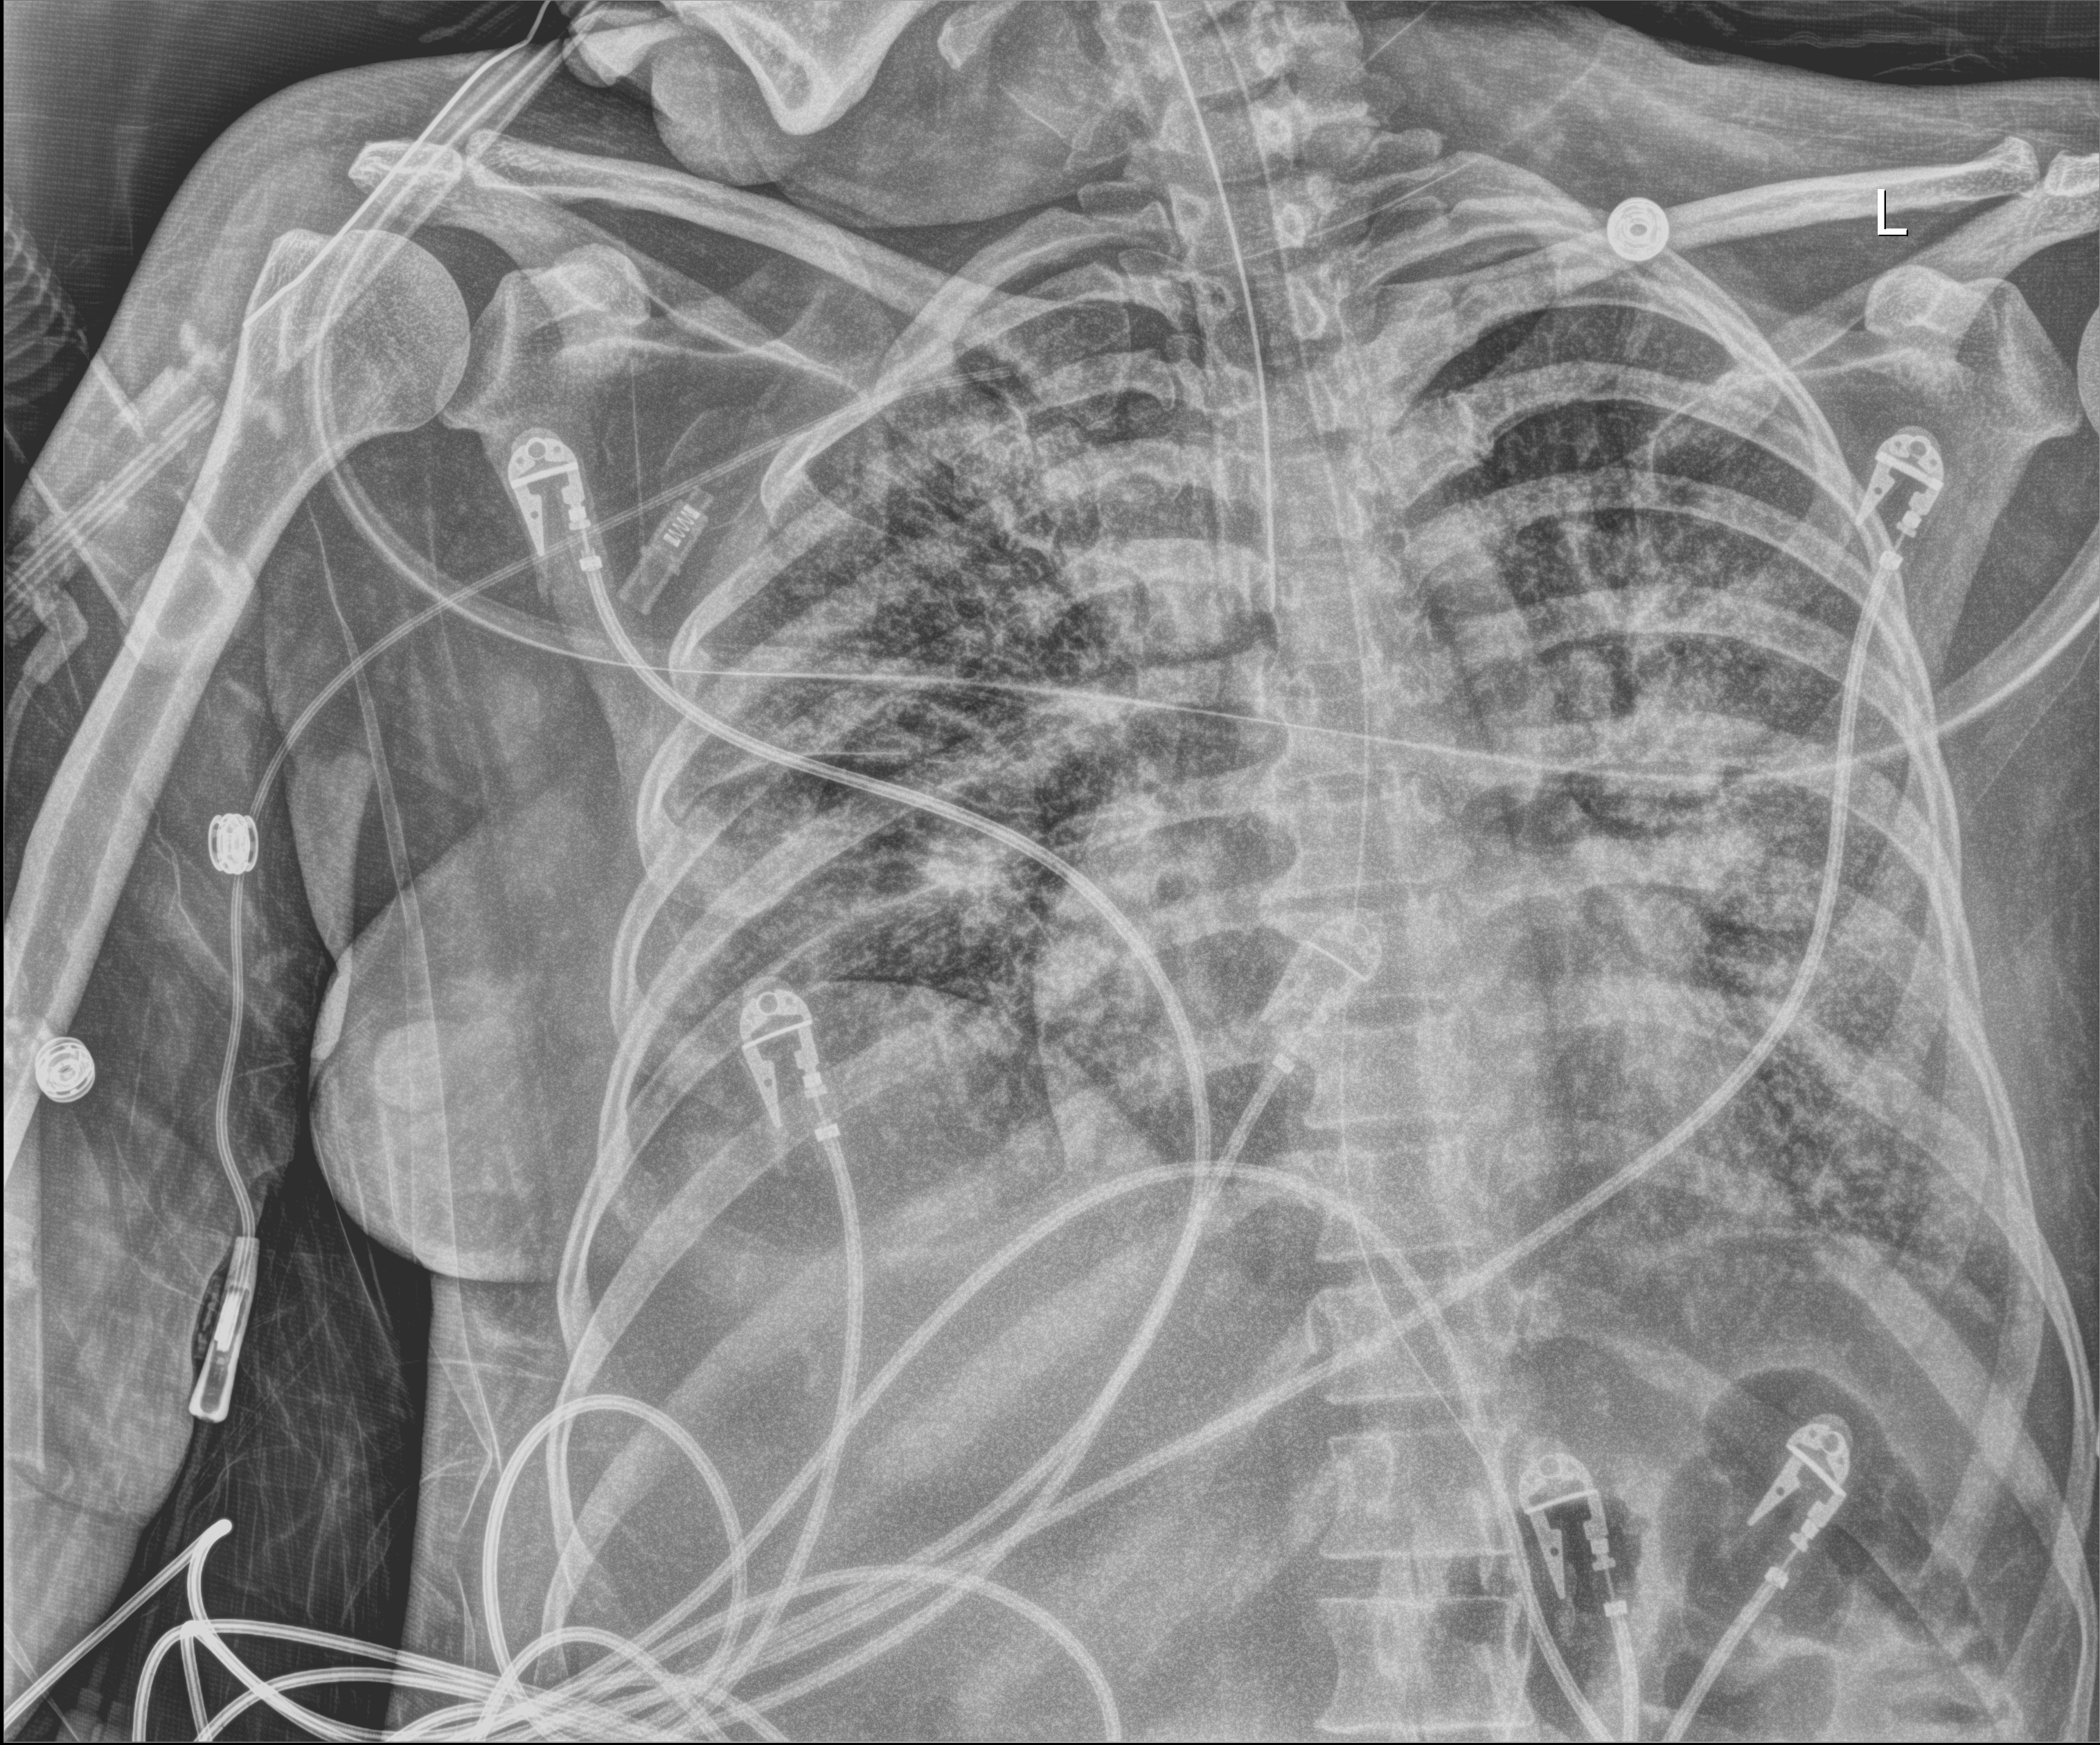
Portable chest radiograph, anteroposterior (AP) projection. Patient hospitalised with COVID-19; female, aged 18–59 years.
Hospital-stay facts (about this admission, not read from this image; timing relative to this image not recorded): admitted to intensive care during this hospital stay: yes.